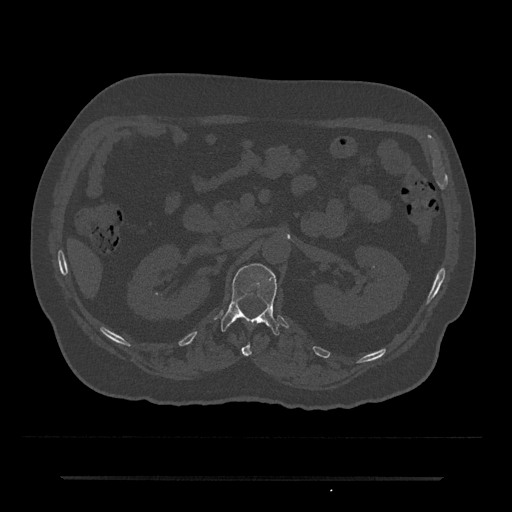
CT including the spine, one axial slice; slice 80 of 797 in the series (ordered by position); reconstruction kernel Br40s/3; bone window (W 1800 / L 400 HU); 0.5 mm slice thickness; 512 × 512 image matrix, field of view 437 × 437 mm. Male patient, age 69 years. From the clinical record (not read from this slice): primary cancer: prostate.
Outlined on this slice (semi-automatically segmented with operator editing):
- L1 vertebra: bounding box [x1, y1, x2, y2] px = [221, 263, 279, 336]
- T12 vertebra: [241, 343, 252, 356]